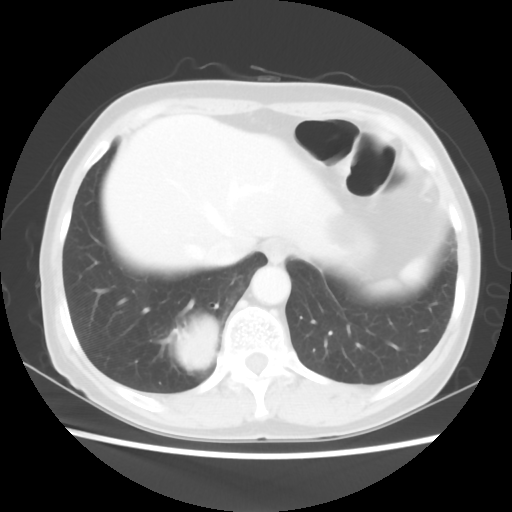
Chest CT, one axial slice. Position 11 of 56 along the scan axis. 120 kVp. Lung window (W 1500 / L -600 HU). 512 × 512 image matrix, field of view 332 × 332 mm. Patient: female, 66 years. From the clinical record (not read from this slice): clinical TNM (as recorded): T2 N3 M0; histopathological grade: G3.
Structures marked on this image (rectangle marked by the reading radiologist):
- lung tumour (recorded histology: small cell carcinoma): bounding box (x1, y1, x2, y2) in pixels: (162, 308, 221, 373)